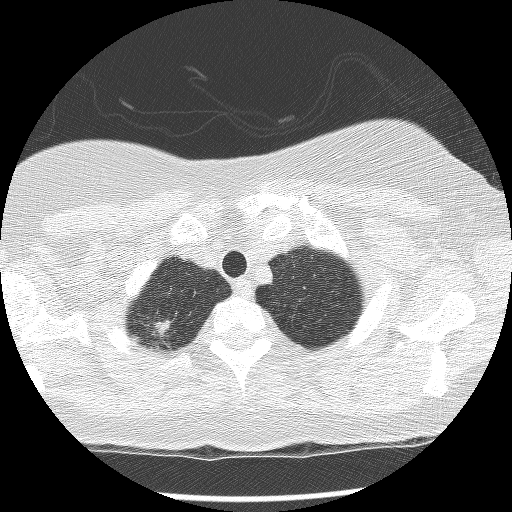
Low-dose screening chest CT, axial slice. Second screening round (one year after baseline). Lung window (W 1500 / L -600 HU). 2.5 mm slice thickness. Lung (sharp) reconstruction kernel (BONE). Female, age 56 years at enrolment. Current smoker at enrolment.
• Expert-annotated lung lesion, bounding box (x1, y1, x2, y2) in pixels: (127, 310, 182, 359).
• Screening reader's record for this exam: no non-calcified nodule ≥4 mm recorded.
• Official screen result: negative screen, minor abnormalities not suspicious for lung cancer.